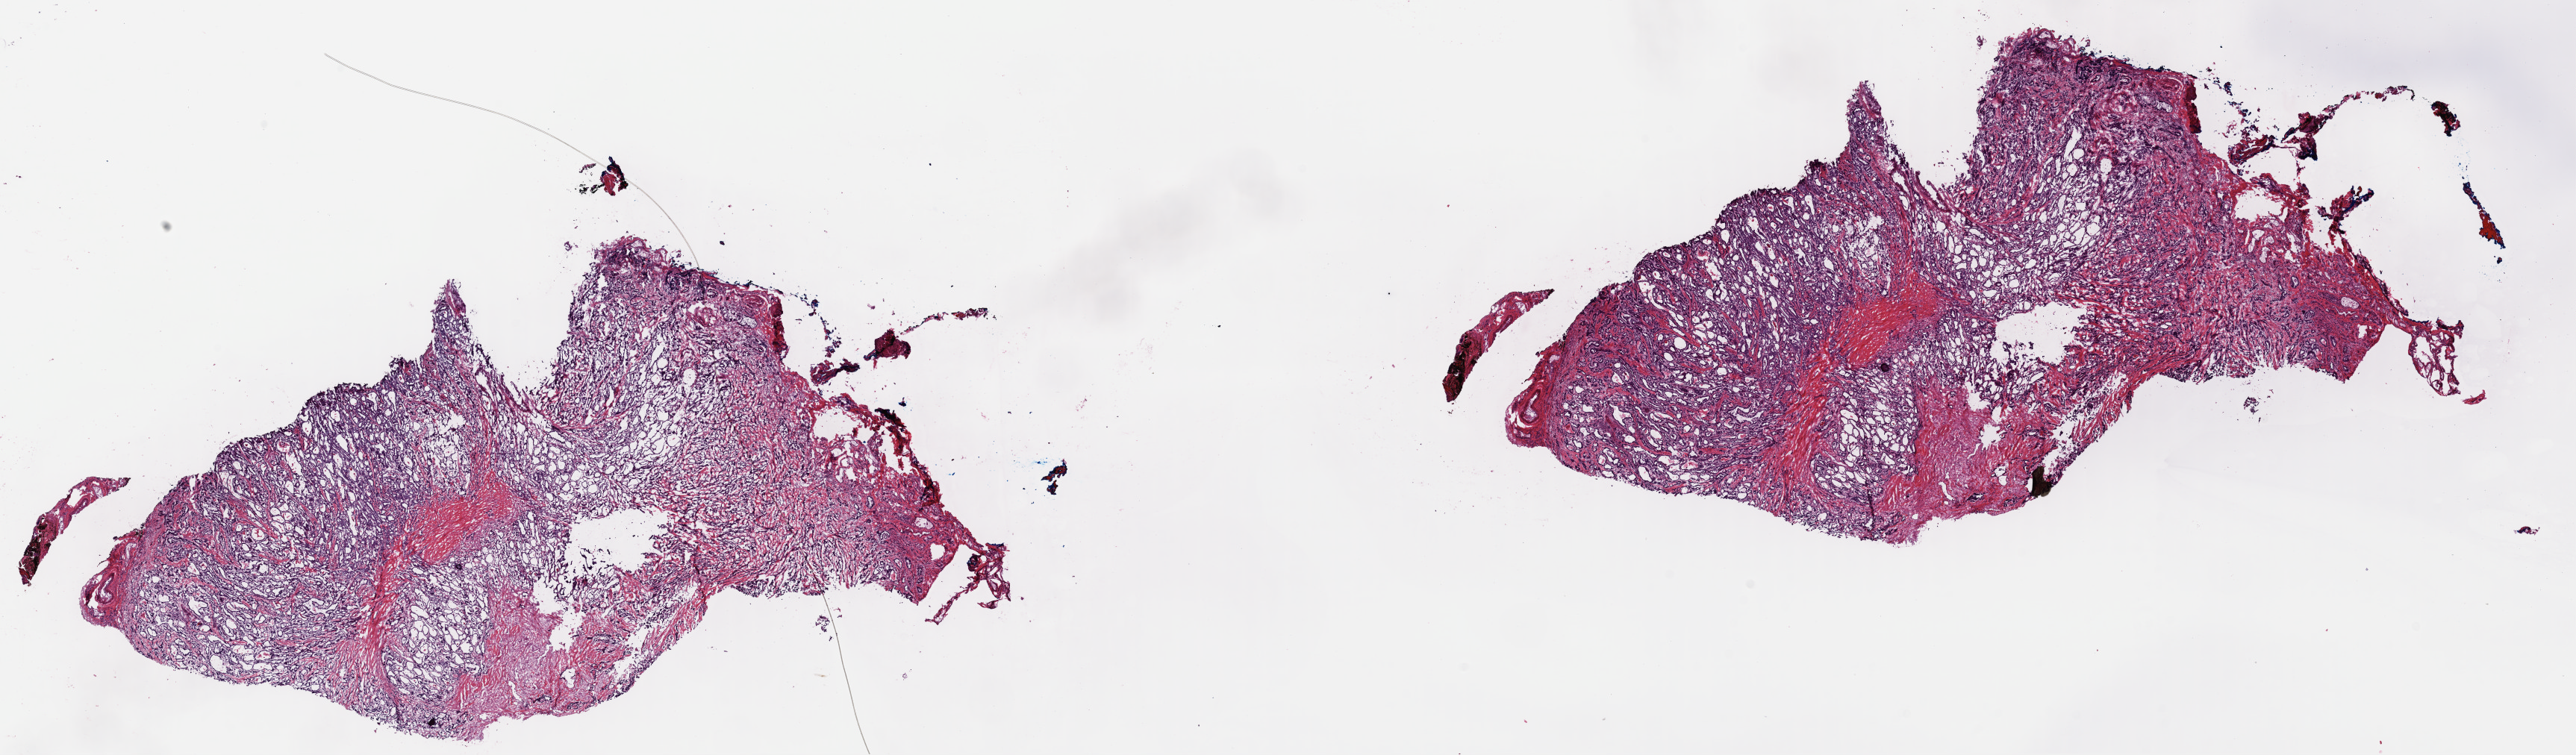
Digitized H&E tissue section (whole slide), a low-resolution overview of the entire scanned area, about 27.3 x 8.0 mm, frozen section from the top of the tissue portion, primary tumour sample from the thyroid. Female, age 38 years at initial diagnosis. Pathologist review of this section (percent, as recorded): tumour cells 85%, tumour nuclei 95%, normal cells 5%, stromal cells 10%, necrosis 0%. Infiltration values recorded for this section: lymphocyte infiltration 0%, monocyte infiltration 1%, neutrophil infiltration 0%.
AJCC pathologic stage: I (7th edition). Laterality: bilateral. Diagnosis: Papillary adenocarcinoma, NOS.